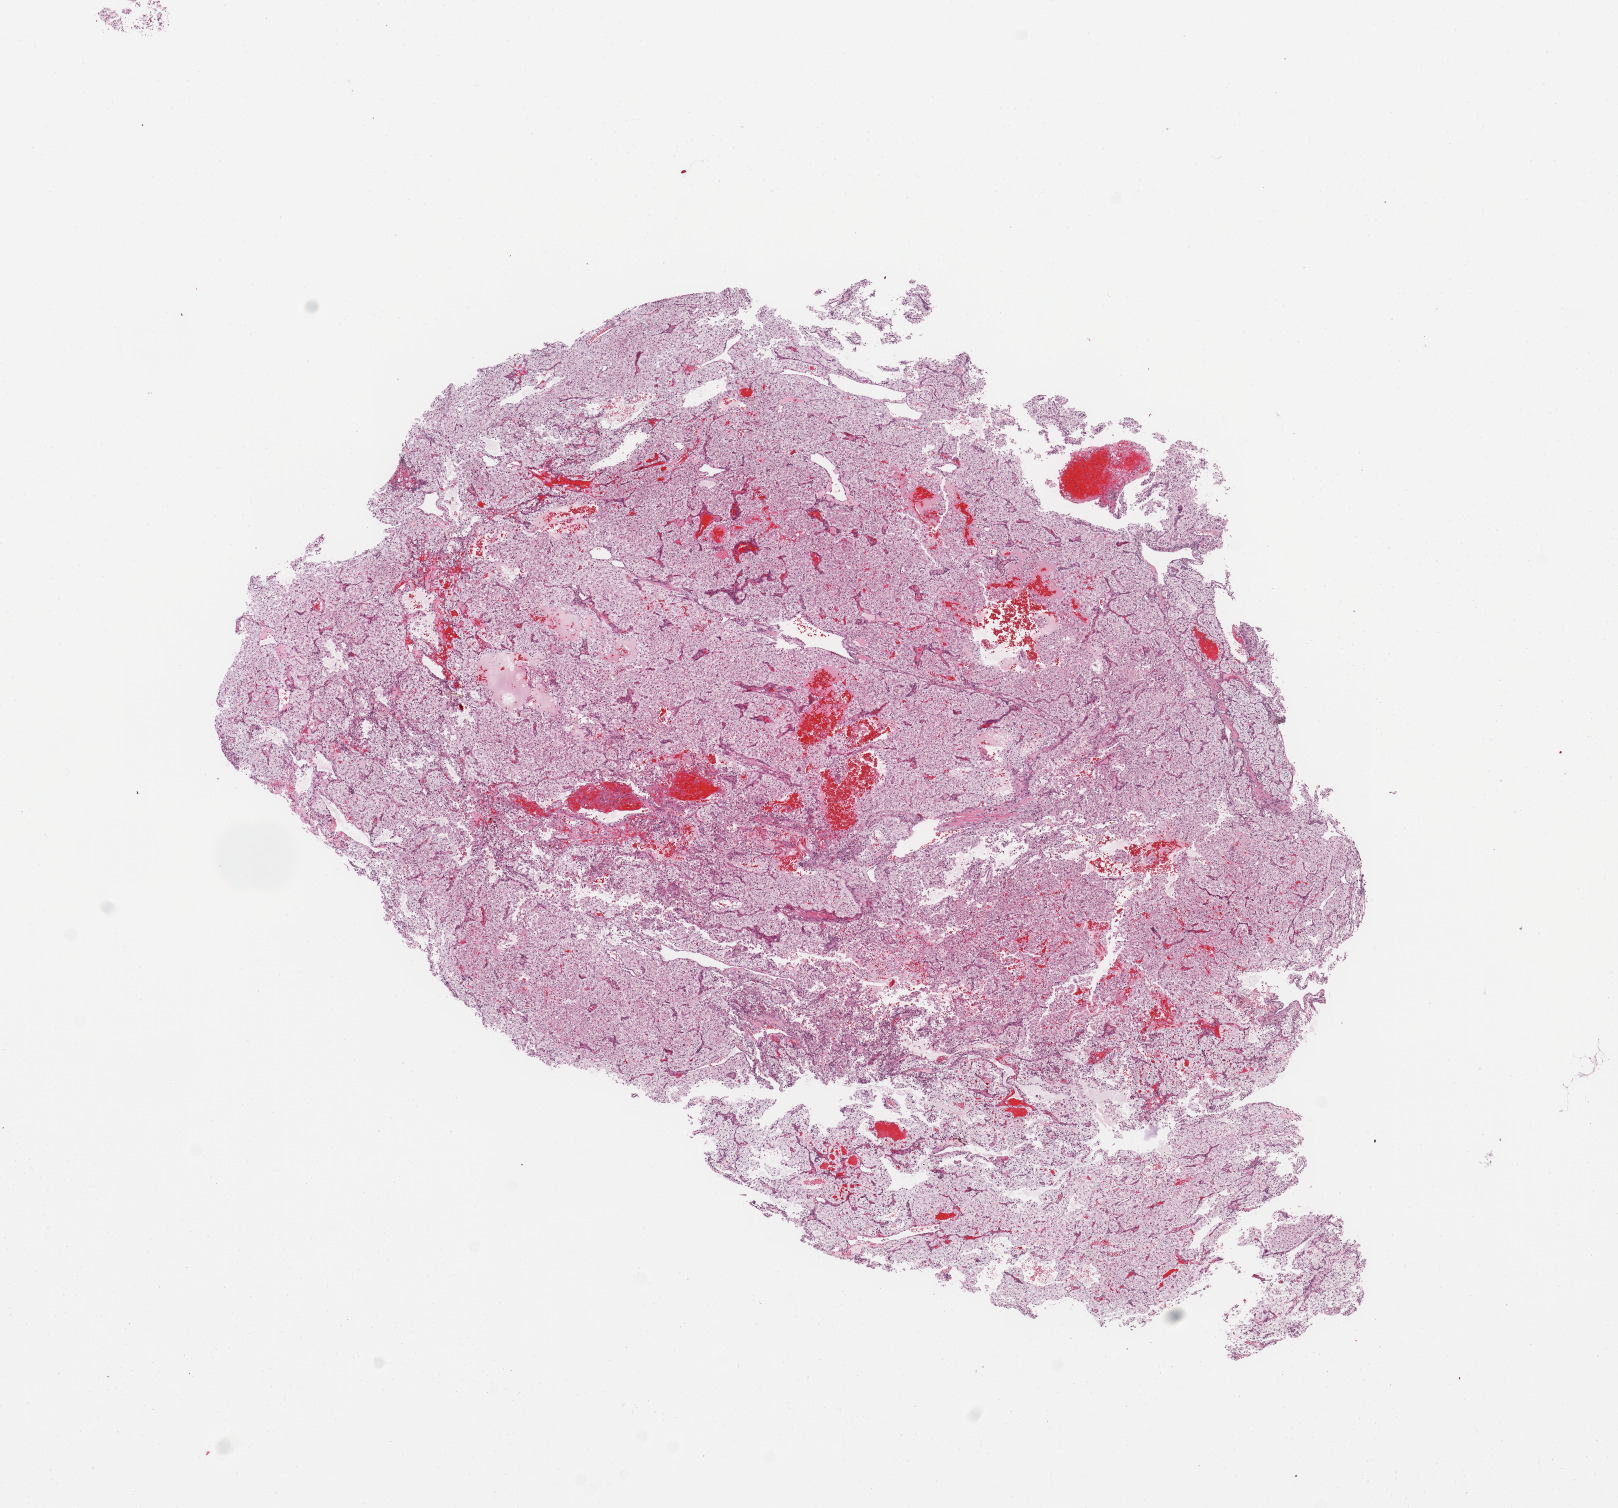
Whole-slide histology image, H&E-stained, whole scanned area (about 12.8 x 11.9 mm) shown as a low-resolution overview, kidney, tumour tissue. 57-year-old female patient. Histologic grade: G3 (poorly differentiated).
* AJCC pathologic stage: III
* primary tumour site (as recorded): middle
* histologic diagnosis: Renal cell carcinoma, NOS